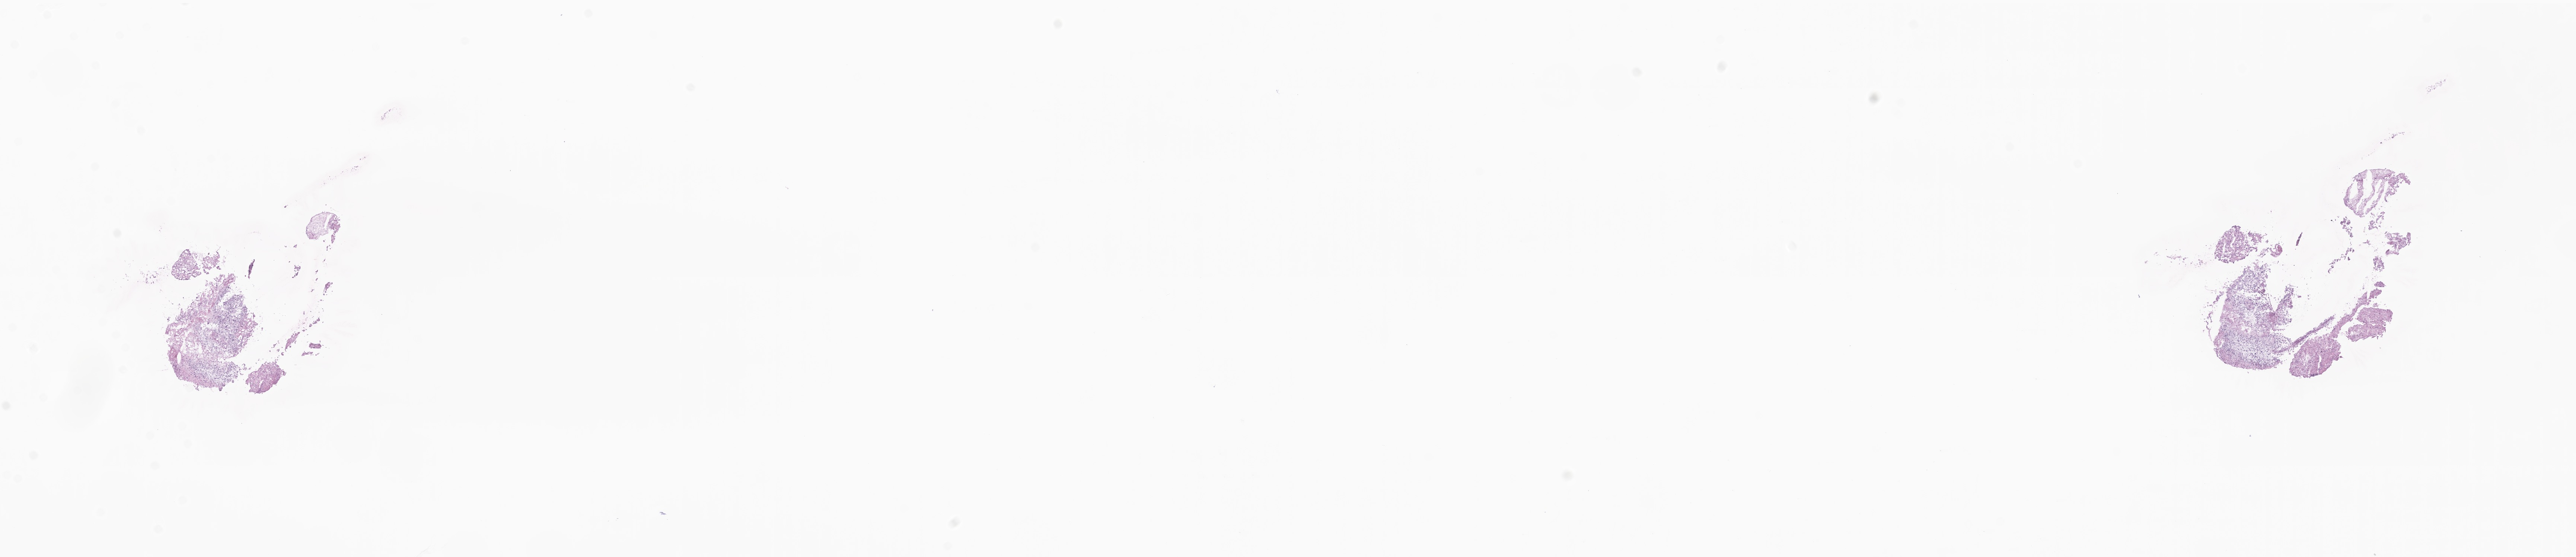
Digitized haematoxylin and eosin-stained section of tumor tissue from the brain, a low-resolution overview of the entire scanned area, about 29.2 x 6.3 mm; frozen section. Male patient, age 90 months.
Diagnosis (ICD-O-3 morphology term): Glioma, malignant.